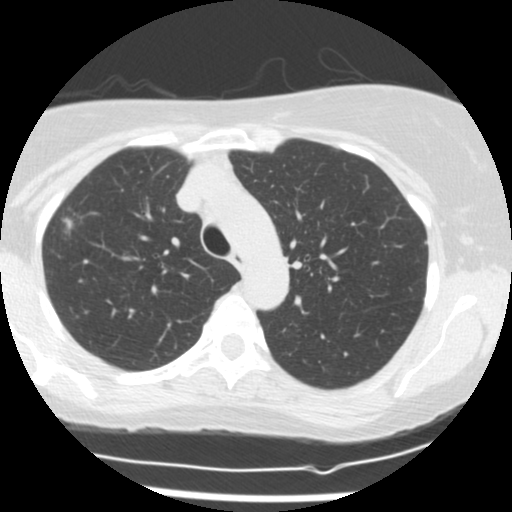
Low-dose screening chest CT, axial slice; baseline annual screen; lung window (W 1500 / L -600 HU); 120 kVp; slice 45 of 160 in the series; 512 × 512 image matrix, field of view 300 × 300 mm. Female participant, aged 58 years at enrolment. Former smoker at enrolment.
Expert reader's lesion annotation, bounding box <42,202,94,239> (left, top, right, bottom; pixels). Screening reader's record for this exam (one nodule recorded; not confirmed to be the boxed lesion): non-calcified nodule or mass ≥4 mm, right upper lobe, 12 × 9 mm, spiculated (stellate) margins, soft tissue attenuation. Official screen result: positive, change unspecified: nodule(s) >= 4 mm or enlarging nodule(s), mass(es), or other non-specific abnormalities suspicious for lung cancer. Participant outcome: lung cancer diagnosed 21 days after this screen — adenocarcinoma, NOS, right upper lobe, moderately differentiated (G2), stage IA (AJCC 6th edition), 10 mm at pathology.